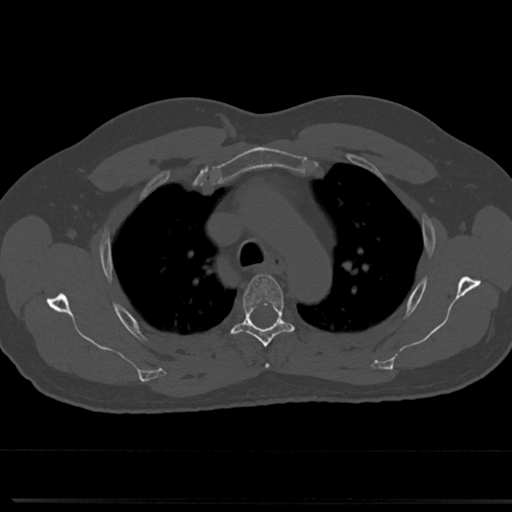
CT including the spine, one axial slice; reconstruction kernel Br40s/3; 120 kVp; bone window (W 1800 / L 400 HU); 512 × 512 image matrix, field of view 355 × 355 mm. Patient: male, 61 years. Case-level facts recorded for this patient, not image findings: primary cancer: prostate.
Outlined on this slice (semi-automatically segmented with operator editing):
- T3 vertebra: bounding box (x1, y1, x2, y2) in pixels: (265, 363, 269, 368)
- T4 vertebra: (232, 274, 295, 347)